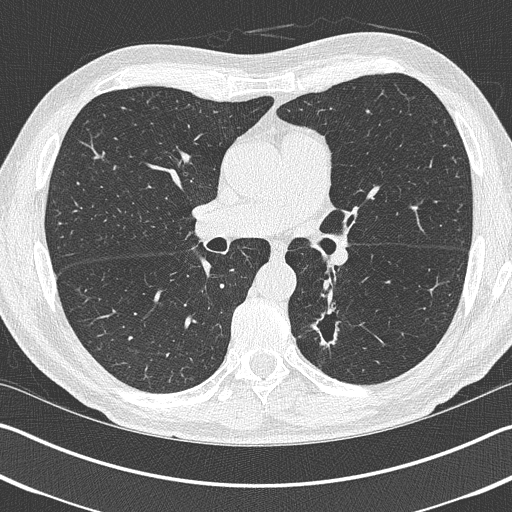
Axial slice from a low-dose chest CT screening exam. Baseline annual screen. Lung window (W 1500 / L -600 HU). 1 mm slice thickness. Male, age 69 years at enrolment. Current smoker at enrolment.
Expert reader's lesion annotation, bounding box <296,306,352,362> (left, top, right, bottom; pixels). Screening reader's record for this exam (one nodule recorded; not confirmed to be the boxed lesion): non-calcified nodule or mass ≥4 mm, left upper lobe, 19 × 19 mm, spiculated (stellate) margins, pre-existing on the prior screen: yes. Later outcome: lung cancer diagnosed 202 days after this screen — non-small cell carcinoma, left lower lobe, stage IIIA (AJCC 6th edition), 20 mm at pathology.